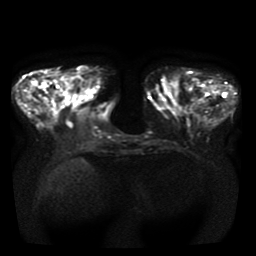
Breast MRI, one axial slice. Slice 11 of 41 in the series (ordered by position). Diffusion-weighted series; image 2 of 4 stored at this slice position (different b-values; order by instance number). 1.5 T. 5 mm slice thickness. 256 × 256 image matrix. Female patient.
Outlined on this slice (outlined manually by an expert reader):
- tumour on diffusion-weighted imaging: bounding box [x1, y1, x2, y2] px = [37, 83, 49, 89]